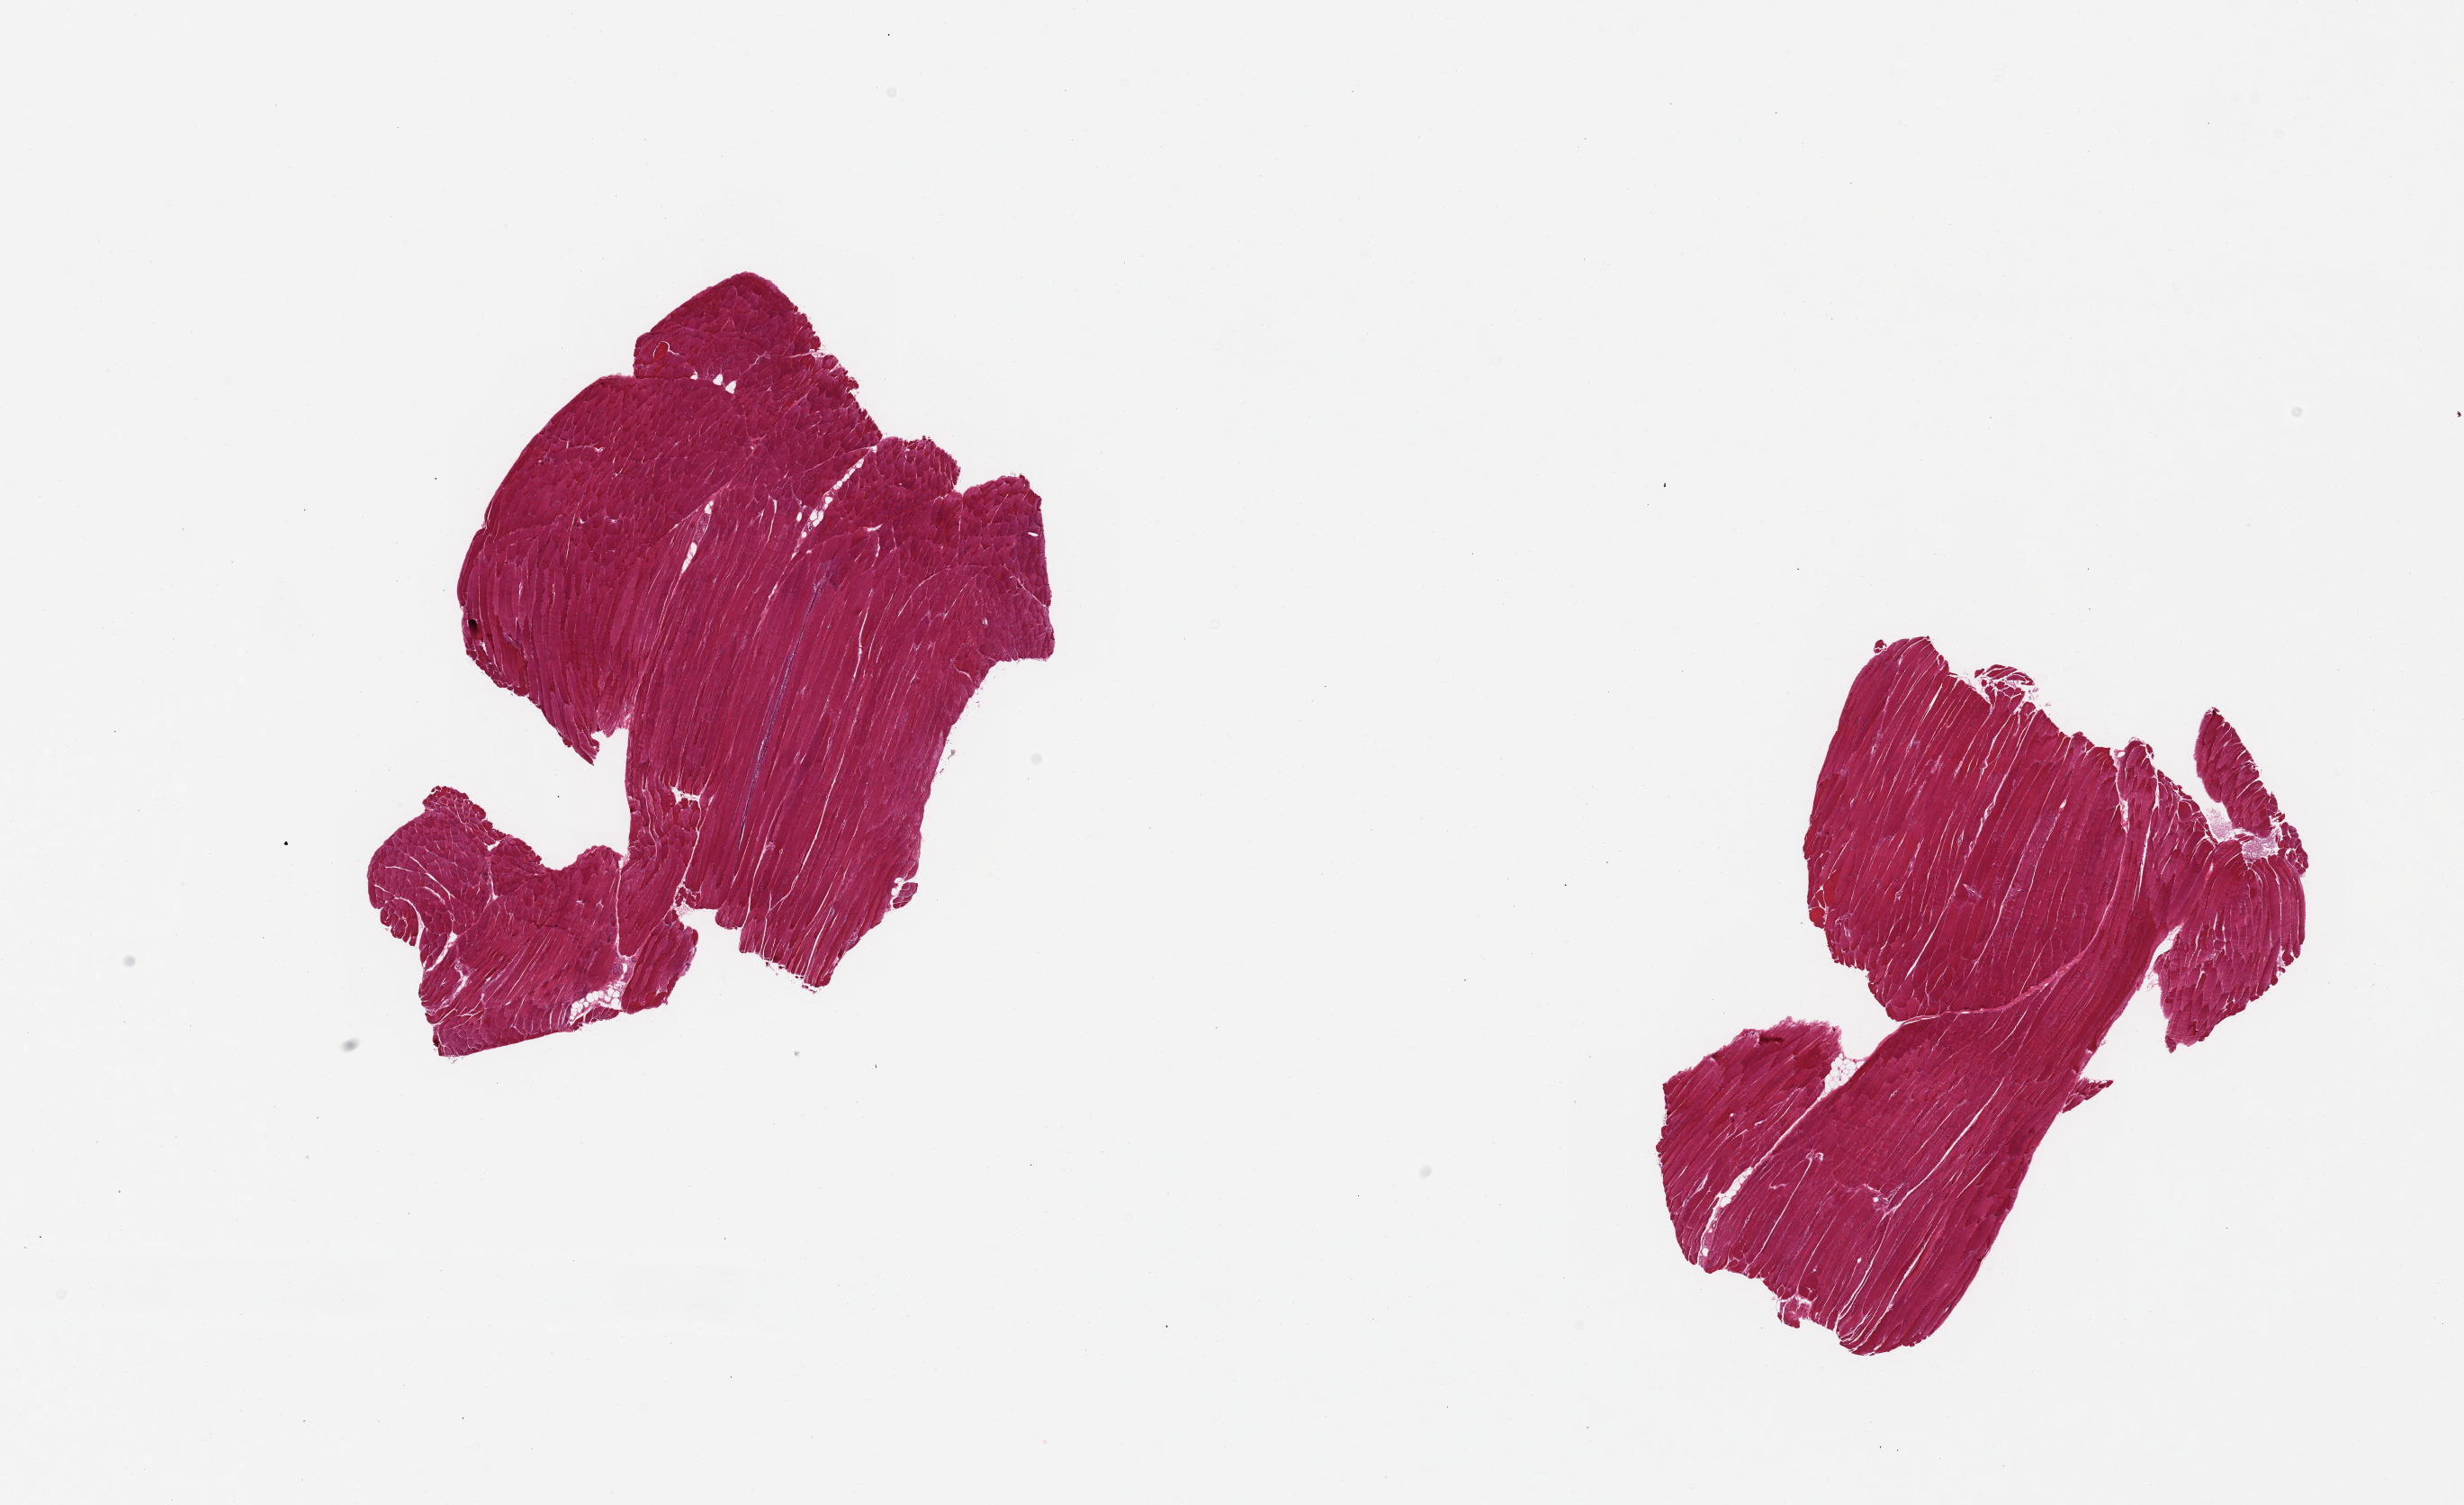
Whole-slide image, haematoxylin and eosin stain — low-resolution overview of the scanned area, about 21.7 x 13.2 mm, PAXgene-fixed, paraffin-embedded tissue, sampled site (target tissue): skeletal muscle, tissue donor sample.
- review note (as recorded): 2 pieces, trace interstitial fat